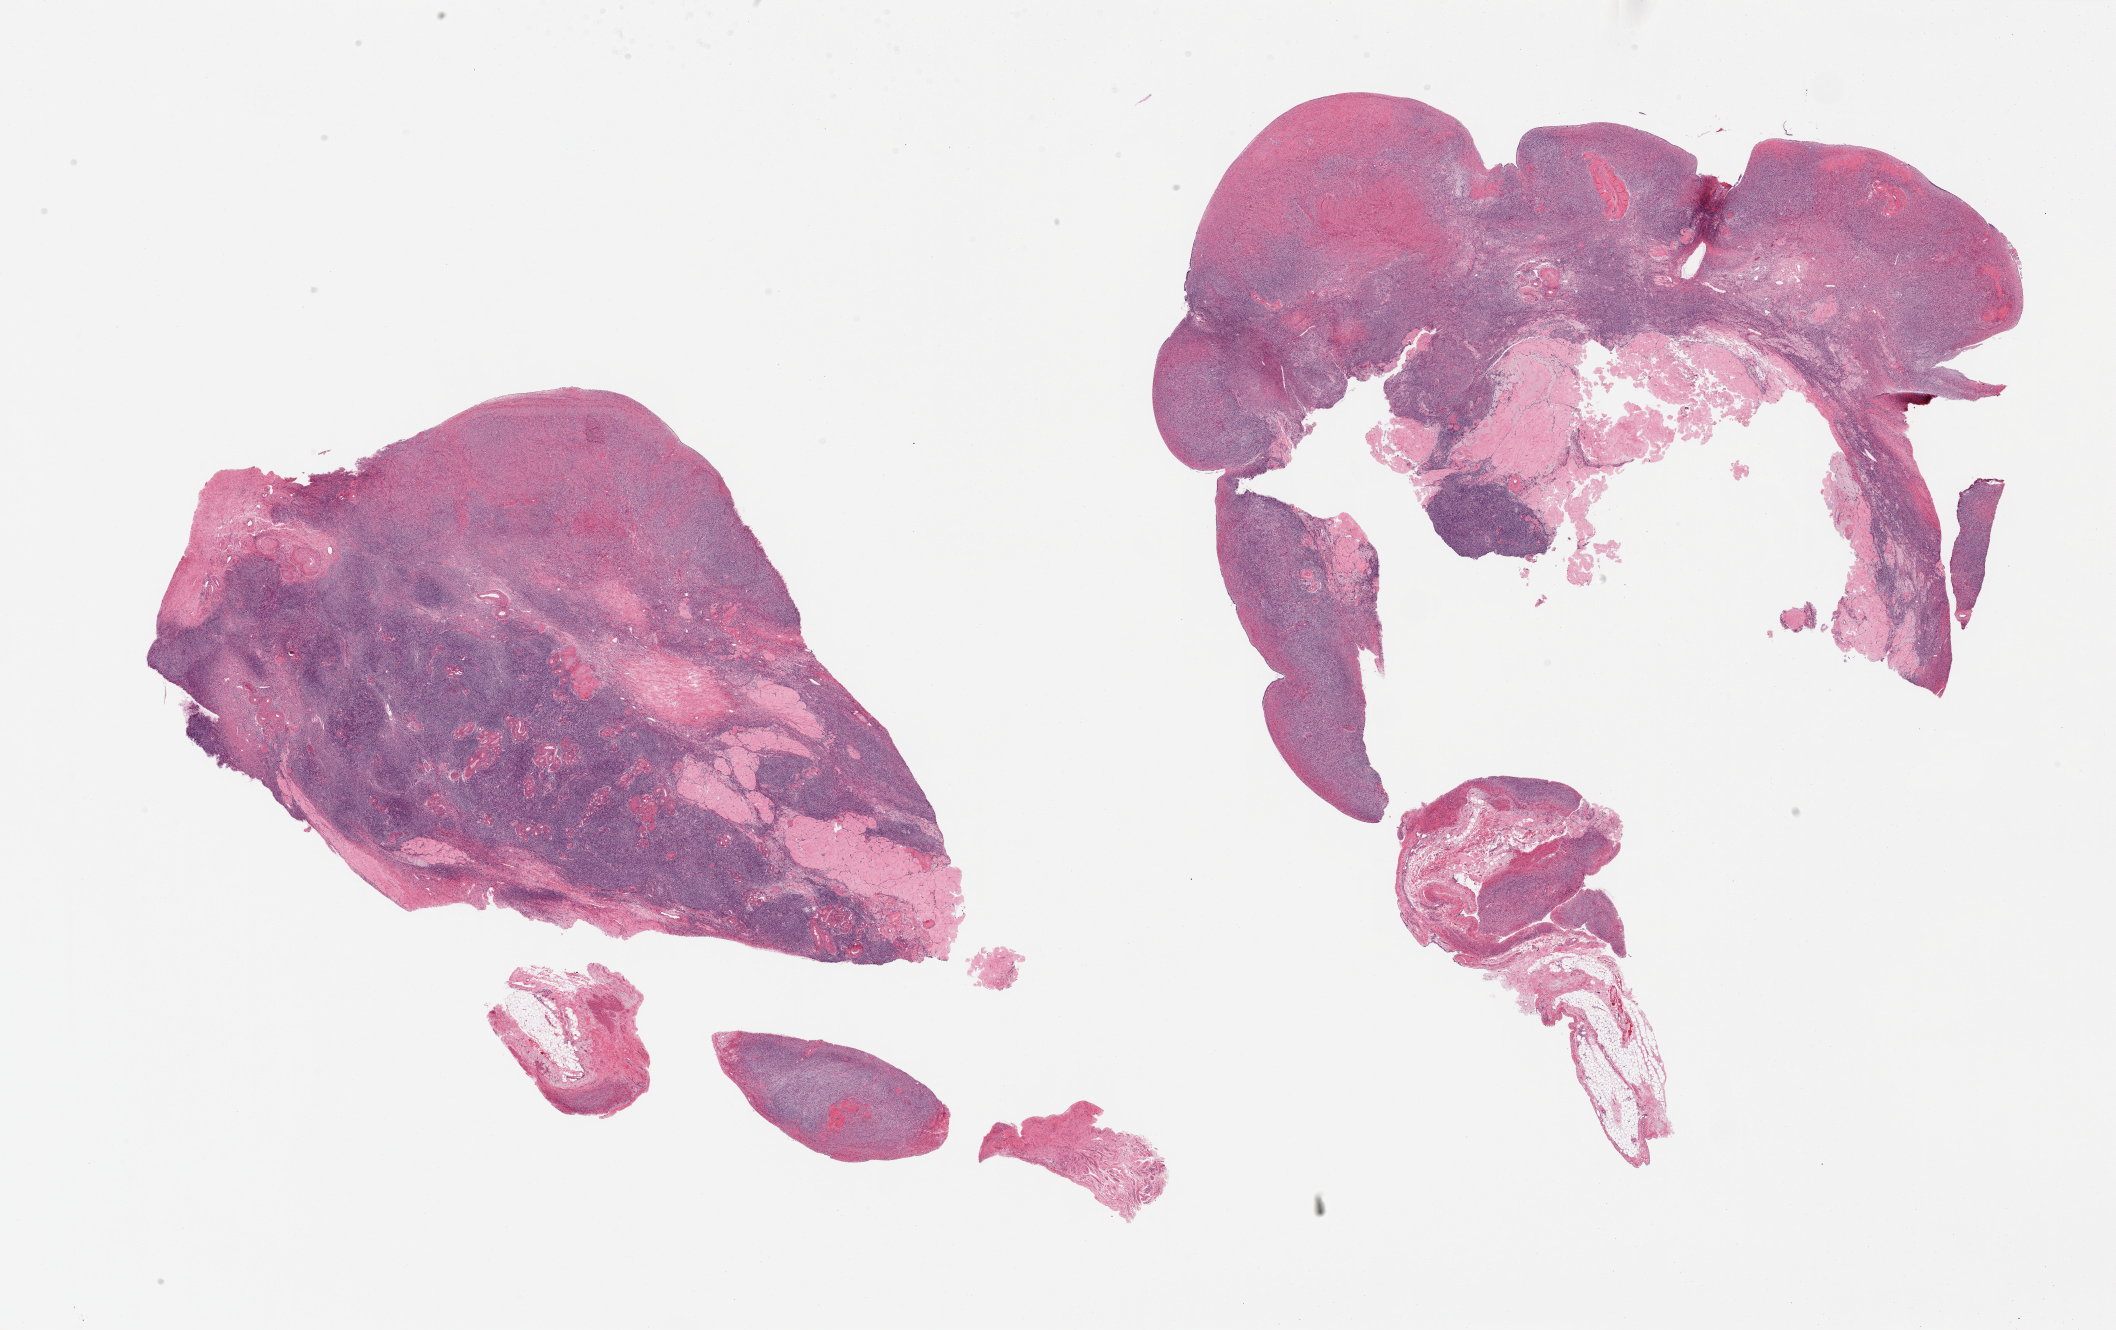
H&E whole-slide image, brightfield, low-resolution overview of the scanned area, about 33.5 x 21.0 mm. PAXgene-fixed paraffin-embedded (PFPE) section. Target tissue: ovary. Tissue donor sample. Female donor.
Pathologist's review note for this sample: 2 pieces + fragments, corpora albicantia present.